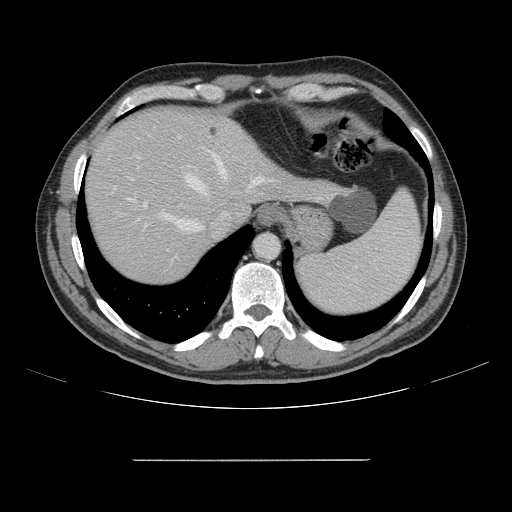
Contrast-enhanced abdominal CT, one axial slice; position 127 of 164 along the scan axis; 120 kVp; intravenous contrast given; soft-tissue window (W 400 / L 40 HU); 2.5 mm slice thickness; 512 × 512 image matrix, field of view 404 × 404 mm. Male patient, age 54 years. Case-level facts recorded for this patient, not image findings: diagnosis: colorectal cancer liver metastases, imaged before liver resection; multiple liver metastases: yes; largest metastasis: 1 cm.
Outlined on this slice (manually delineated by an expert):
- hepatic veins: box from (x=138, y=154) to (x=264, y=232) px
- liver: (x=87, y=108)–(x=334, y=283)
- planned liver remnant (the part of the liver to remain after resection): (x=87, y=108)–(x=255, y=282)
- portal vein (with intrahepatic branches): (x=130, y=156)–(x=147, y=227)